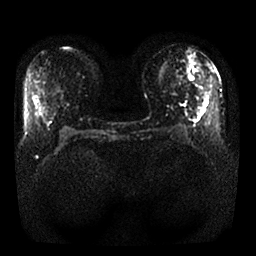
Breast MRI, one axial slice. Position 11 of 25 along the scan axis. Diffusion-weighted series; image 2 of 4 stored at this slice position (different b-values; order by instance number). 1.5 T. 4 mm slice thickness. 256 × 256 image matrix. Female patient.
Outlined on this slice (manually delineated by an expert):
- tumour on diffusion-weighted imaging: bounding box [x1, y1, x2, y2] px = [189, 74, 193, 80]